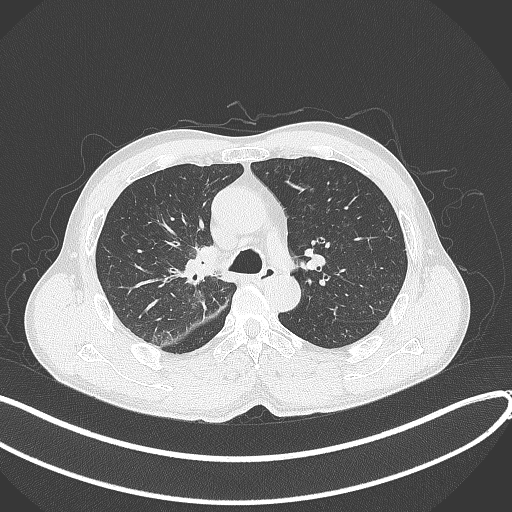
Chest CT, one axial slice; slice 260 of 409 in the series (ordered by position); lung window (W 1500 / L -600 HU); 1 mm slice thickness; 512 × 512 image matrix, field of view 400 × 400 mm. Patient: male, 53 years. Case-level facts recorded for this patient, not image findings: clinical TNM (as recorded): T1b N0 M0.
Structures marked on this image (bounding box drawn by a radiologist):
- lung tumour (recorded histology: squamous cell carcinoma): bounding box (x1, y1, x2, y2) in pixels: (181, 241, 218, 285)